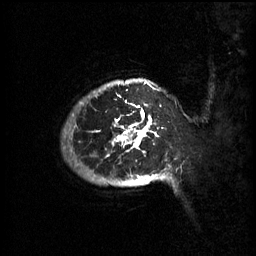
Breast MRI (dynamic contrast-enhanced), one sagittal slice; slice 54 of 60 in the series (ordered by position); 3 images stored at this slice position (order not interpretable as contrast timing); 1.5 T; TE 4.2 ms, TR 11 ms; 256 × 256 image matrix. Patient: female, 51 years.
Outlined on this slice (semi-automatically segmented with operator editing):
- analysis volume of interest (the breast-tissue region the enhancement analysis was run in; not a lesion): bounding box (x1, y1, x2, y2) in pixels: (79, 80, 174, 187)
- tumour enhancement mask (voxels above the 70 % enhancement threshold inside the analysis volume of interest): (96, 82, 166, 185)